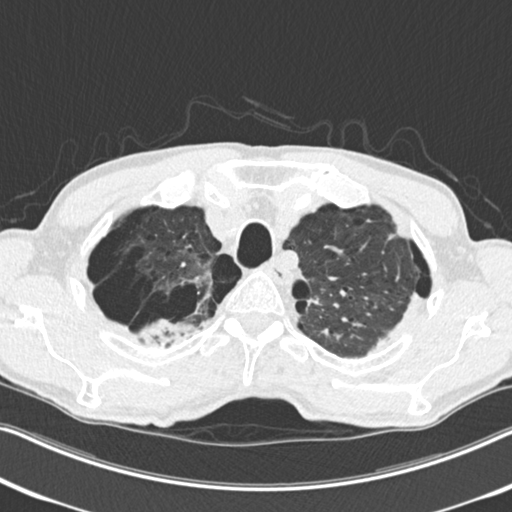
Low-dose screening chest CT, one axial slice; slice 211 of 251 in the series (ordered by position); reconstruction kernel B30f; lung window (W 1500 / L -600 HU); 2 mm slice thickness; 512 × 512 image matrix, field of view 334 × 334 mm.
Annotated regions visible in this slice (outlined manually by an expert reader):
- lesion 1 (tumor, upper lobe of right lung): bounding box [x1, y1, x2, y2] px = [138, 319, 171, 340]